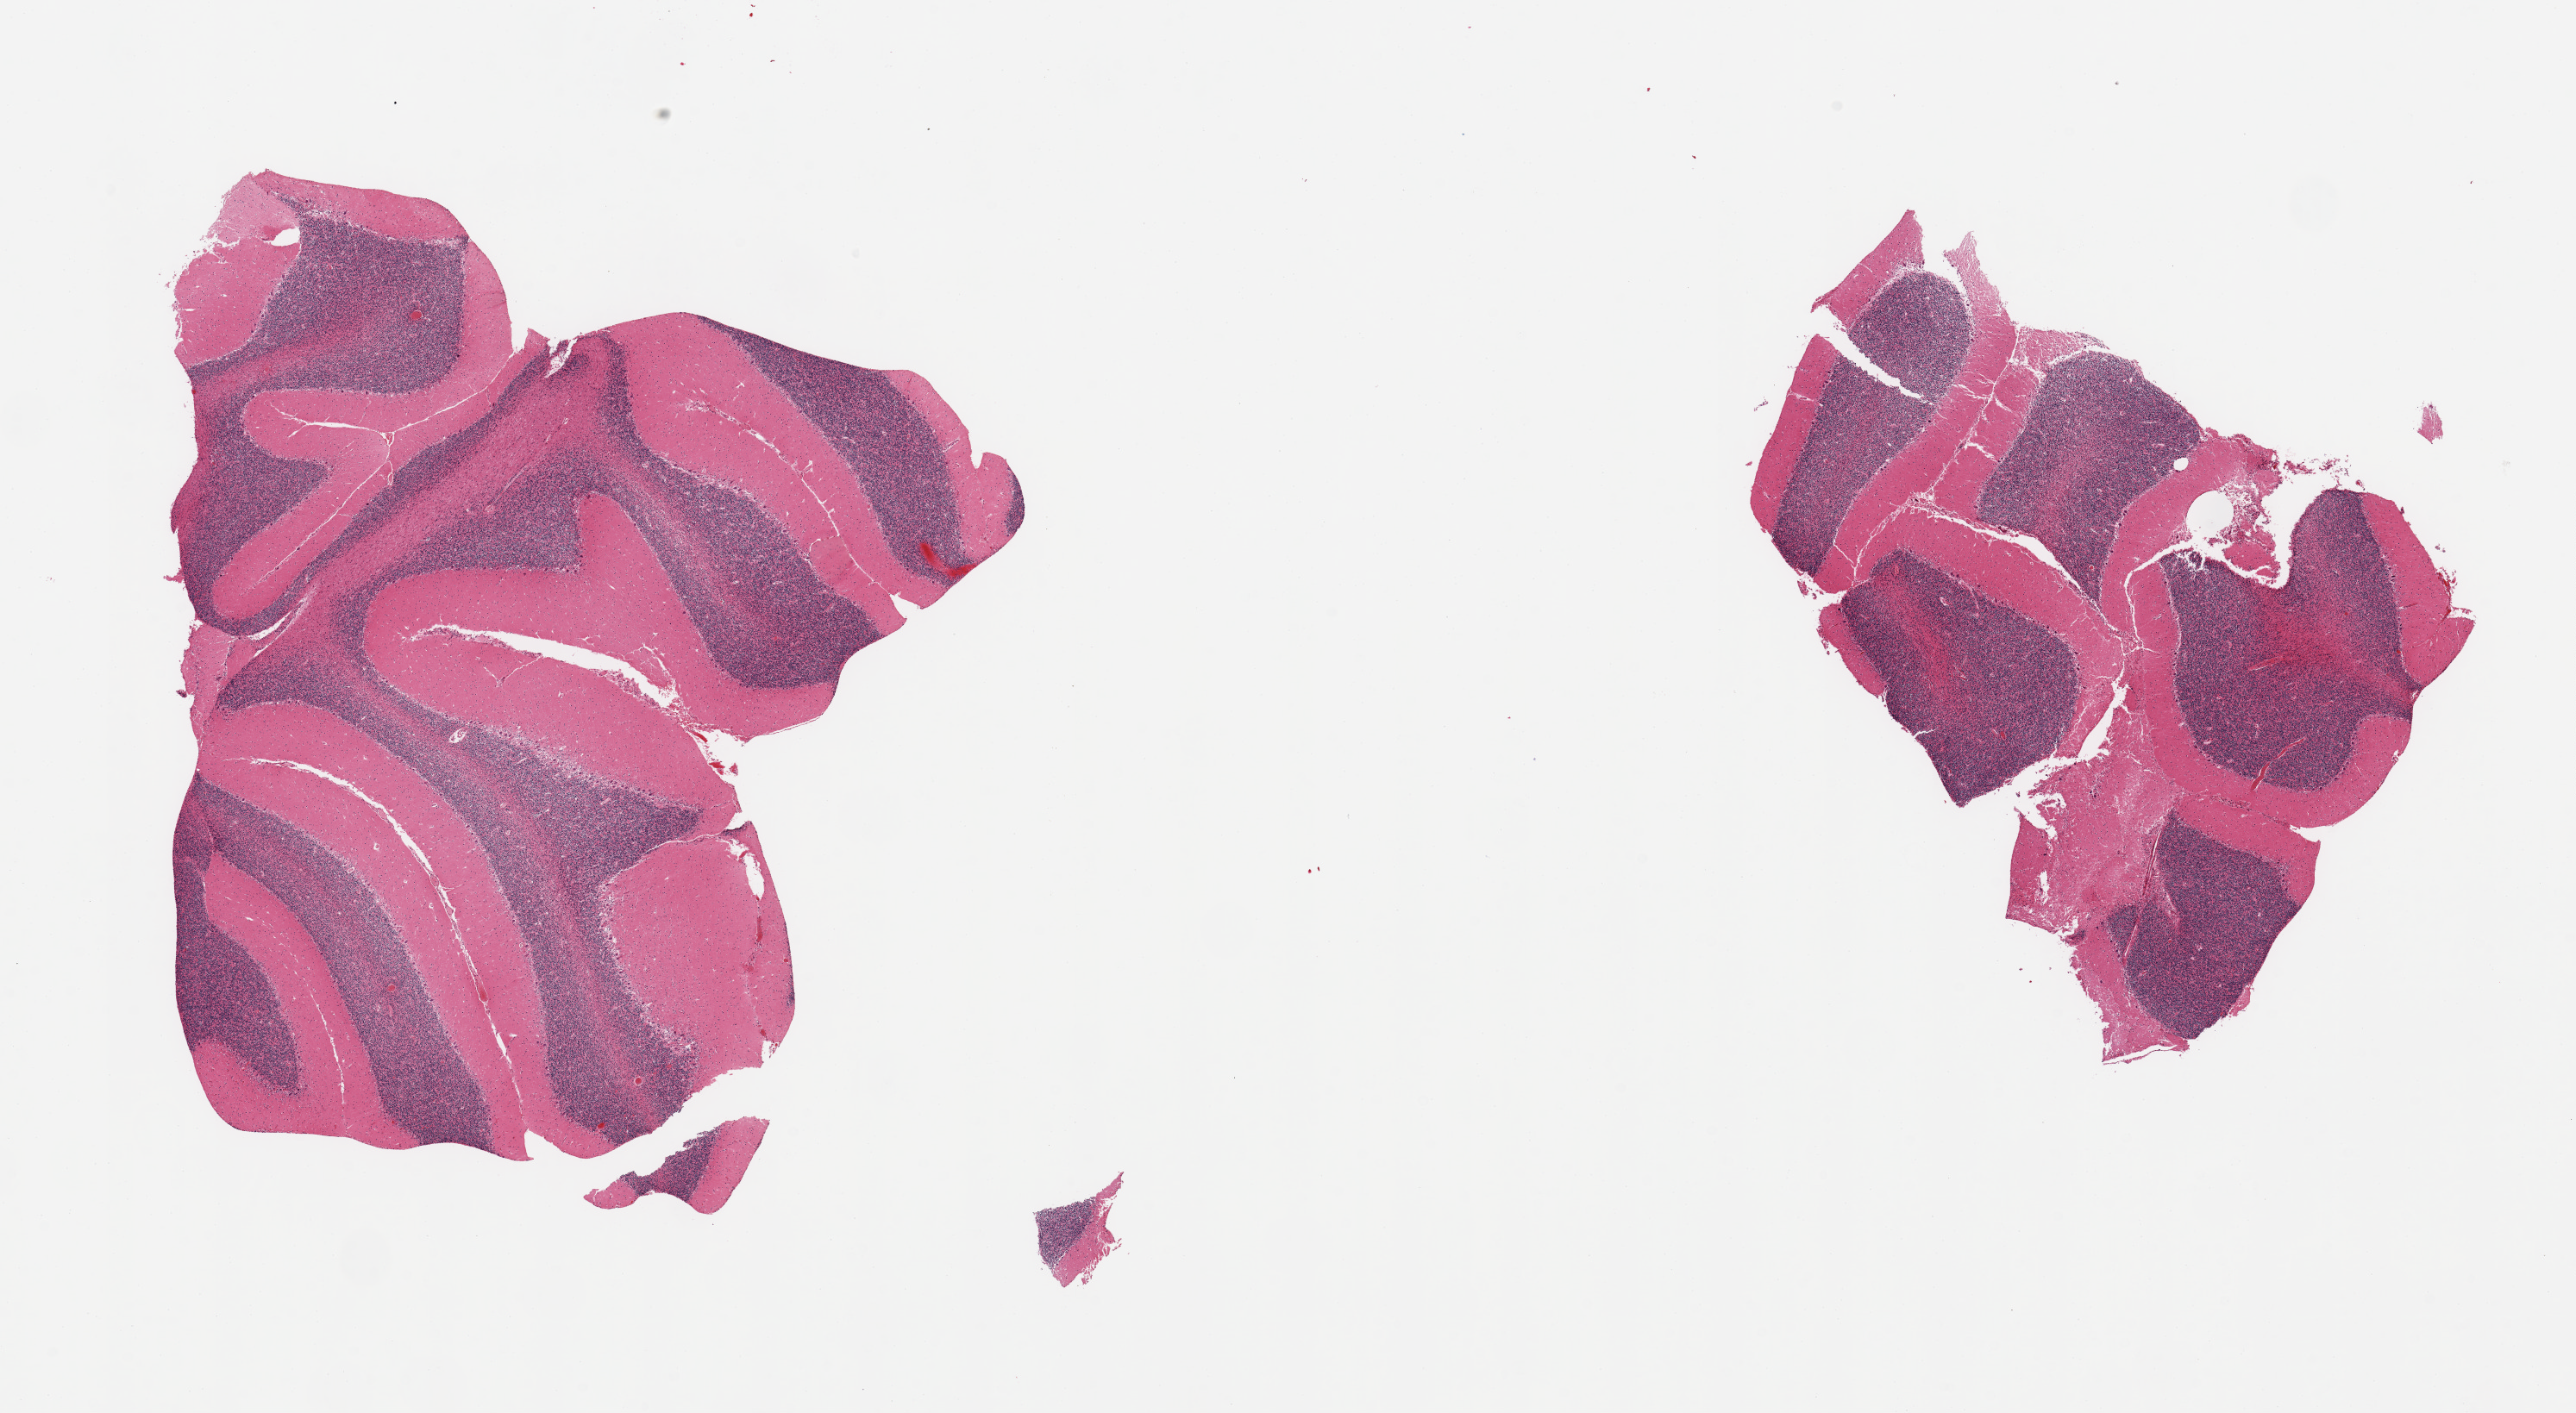
Digitized haematoxylin and eosin-stained section, whole scanned area (about 23.6 x 13.0 mm) shown as a low-resolution overview, PAXgene-fixed paraffin-embedded (PFPE) section, section of cerebellum (target tissue), donor tissue sample. Donor sex: male.
Review note (as recorded): 2 pieces; Purkinje cells well visualized.